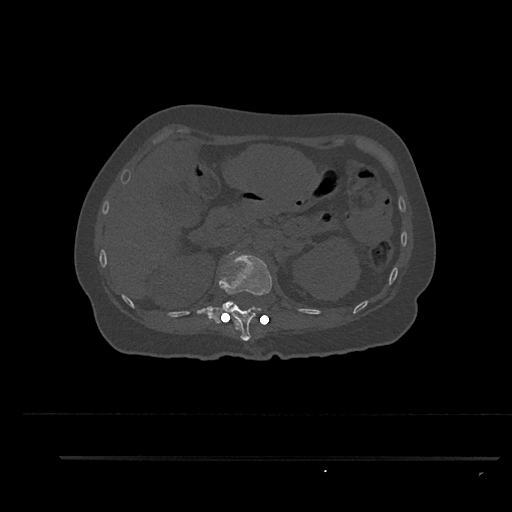
CT including the spine, one axial slice; slice 243 of 797 in the series (ordered by position); reconstruction kernel Br40s/3; bone window (W 1800 / L 400 HU); 512 × 512 image matrix, field of view 408 × 408 mm. Patient: female, 44 years. From the clinical record (not read from this slice): primary cancer: renal; vertebrae with lytic lesions (as recorded): L1.
Outlined on this slice (semi-automatically segmented with operator editing):
- L1 vertebra: bounding box [x1, y1, x2, y2] px = [219, 279, 233, 309]
- T12 vertebra: [200, 251, 272, 341]